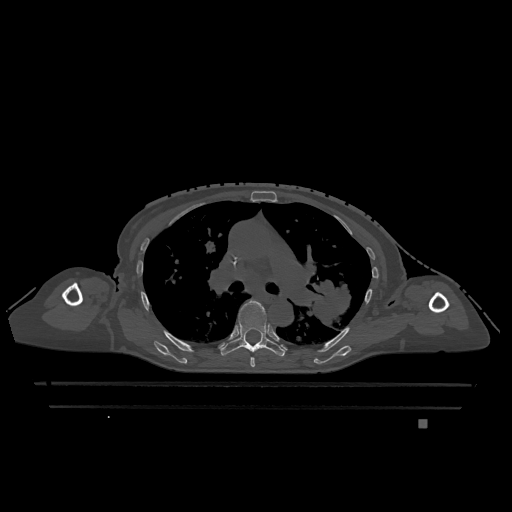
CT including the spine, one axial slice; bone window (W 1800 / L 400 HU); 512 × 512 image matrix, field of view 500 × 500 mm. Patient: female, 74 years. From the clinical record (not read from this slice): primary cancer: lung; vertebrae with lytic lesions (as recorded): T1, T4, T5, T6, L4, L5.
Annotated regions visible in this slice (semi-automatic segmentation, software-assisted and operator-edited):
- T5 vertebra: bounding box [x1, y1, x2, y2] px = [250, 357, 255, 367]
- T6 vertebra: [220, 300, 285, 357]